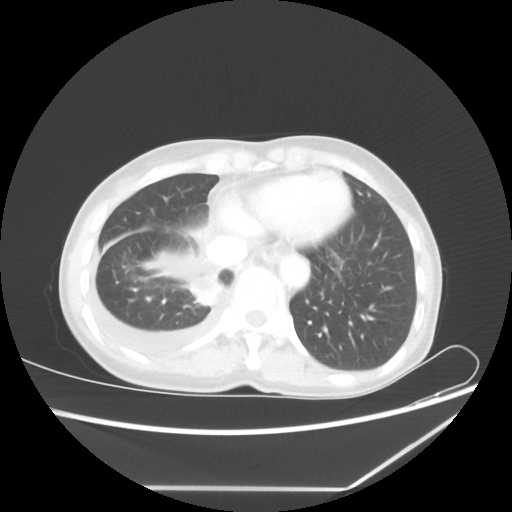
Chest CT, one axial slice. Position 17 of 60 along the scan axis. 80 kVp. Lung window (W 1500 / L -600 HU). 5 mm slice thickness. 512 × 512 image matrix, field of view 364 × 364 mm. Female patient, age 59 years. Case-level facts recorded for this patient, not image findings: clinical TNM (as recorded): T1c N1 M1.
Annotated regions visible in this slice (rectangle marked by the reading radiologist):
- lung tumour (recorded histology: adenocarcinoma): bounding box <189,282,225,307> (left, top, right, bottom; pixels)